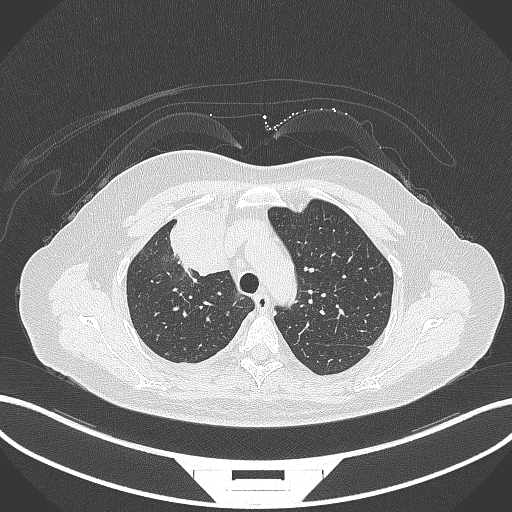
Chest CT, one axial slice; reconstruction kernel B70f; 120 kVp; lung window (W 1500 / L -600 HU); 512 × 512 image matrix, field of view 400 × 400 mm. Female patient, age 52 years. Case-level facts recorded for this patient, not image findings: clinical TNM (as recorded): T3 N1 M1.
Structures marked on this image (bounding box drawn by a radiologist):
- lung tumour (recorded histology: adenocarcinoma): bounding box <165,205,231,281> (left, top, right, bottom; pixels)